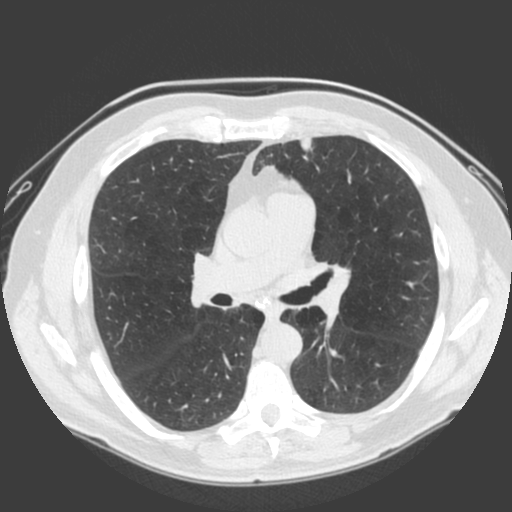
Low-dose screening chest CT, one axial slice; slice 106 of 185 in the series (ordered by position); 120 kVp; lung window (W 1500 / L -600 HU); 2 mm slice thickness; 512 × 512 image matrix.
Outlined on this slice (outlined manually by an expert reader):
- lesion 1 (tumor, lower lobe of left lung): bounding box (x1, y1, x2, y2) in pixels: (300, 137, 313, 151)